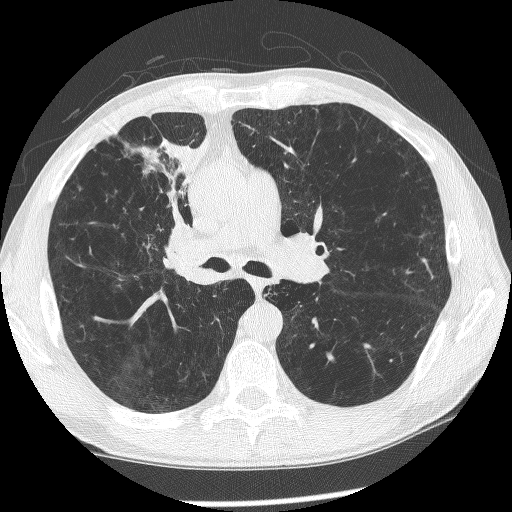
Axial slice from a low-dose chest CT screening exam. Baseline screening round. Lung window (W 1500 / L -600 HU). Male participant, aged 60 years at enrolment. Current smoker at enrolment.
- Expert-annotated lung lesion, bounding box [x1, y1, x2, y2] px = [145, 193, 221, 286].
- Reader record for this screening exam (exam-level; its link to the box is not recorded): non-calcified nodule or mass ≥4 mm, right upper lobe, 12 × 8 mm, spiculated (stellate) margins, mixed attenuation.
- Official screen result: positive, change unspecified: nodule(s) >= 4 mm or enlarging nodule(s), mass(es), or other non-specific abnormalities suspicious for lung cancer.
- Participant outcome: lung cancer diagnosed 208 days after this screen — squamous cell carcinoma, NOS, right upper lobe, right middle lobe, right main stem bronchus, poorly differentiated (G3), stage IV (AJCC 6th edition).